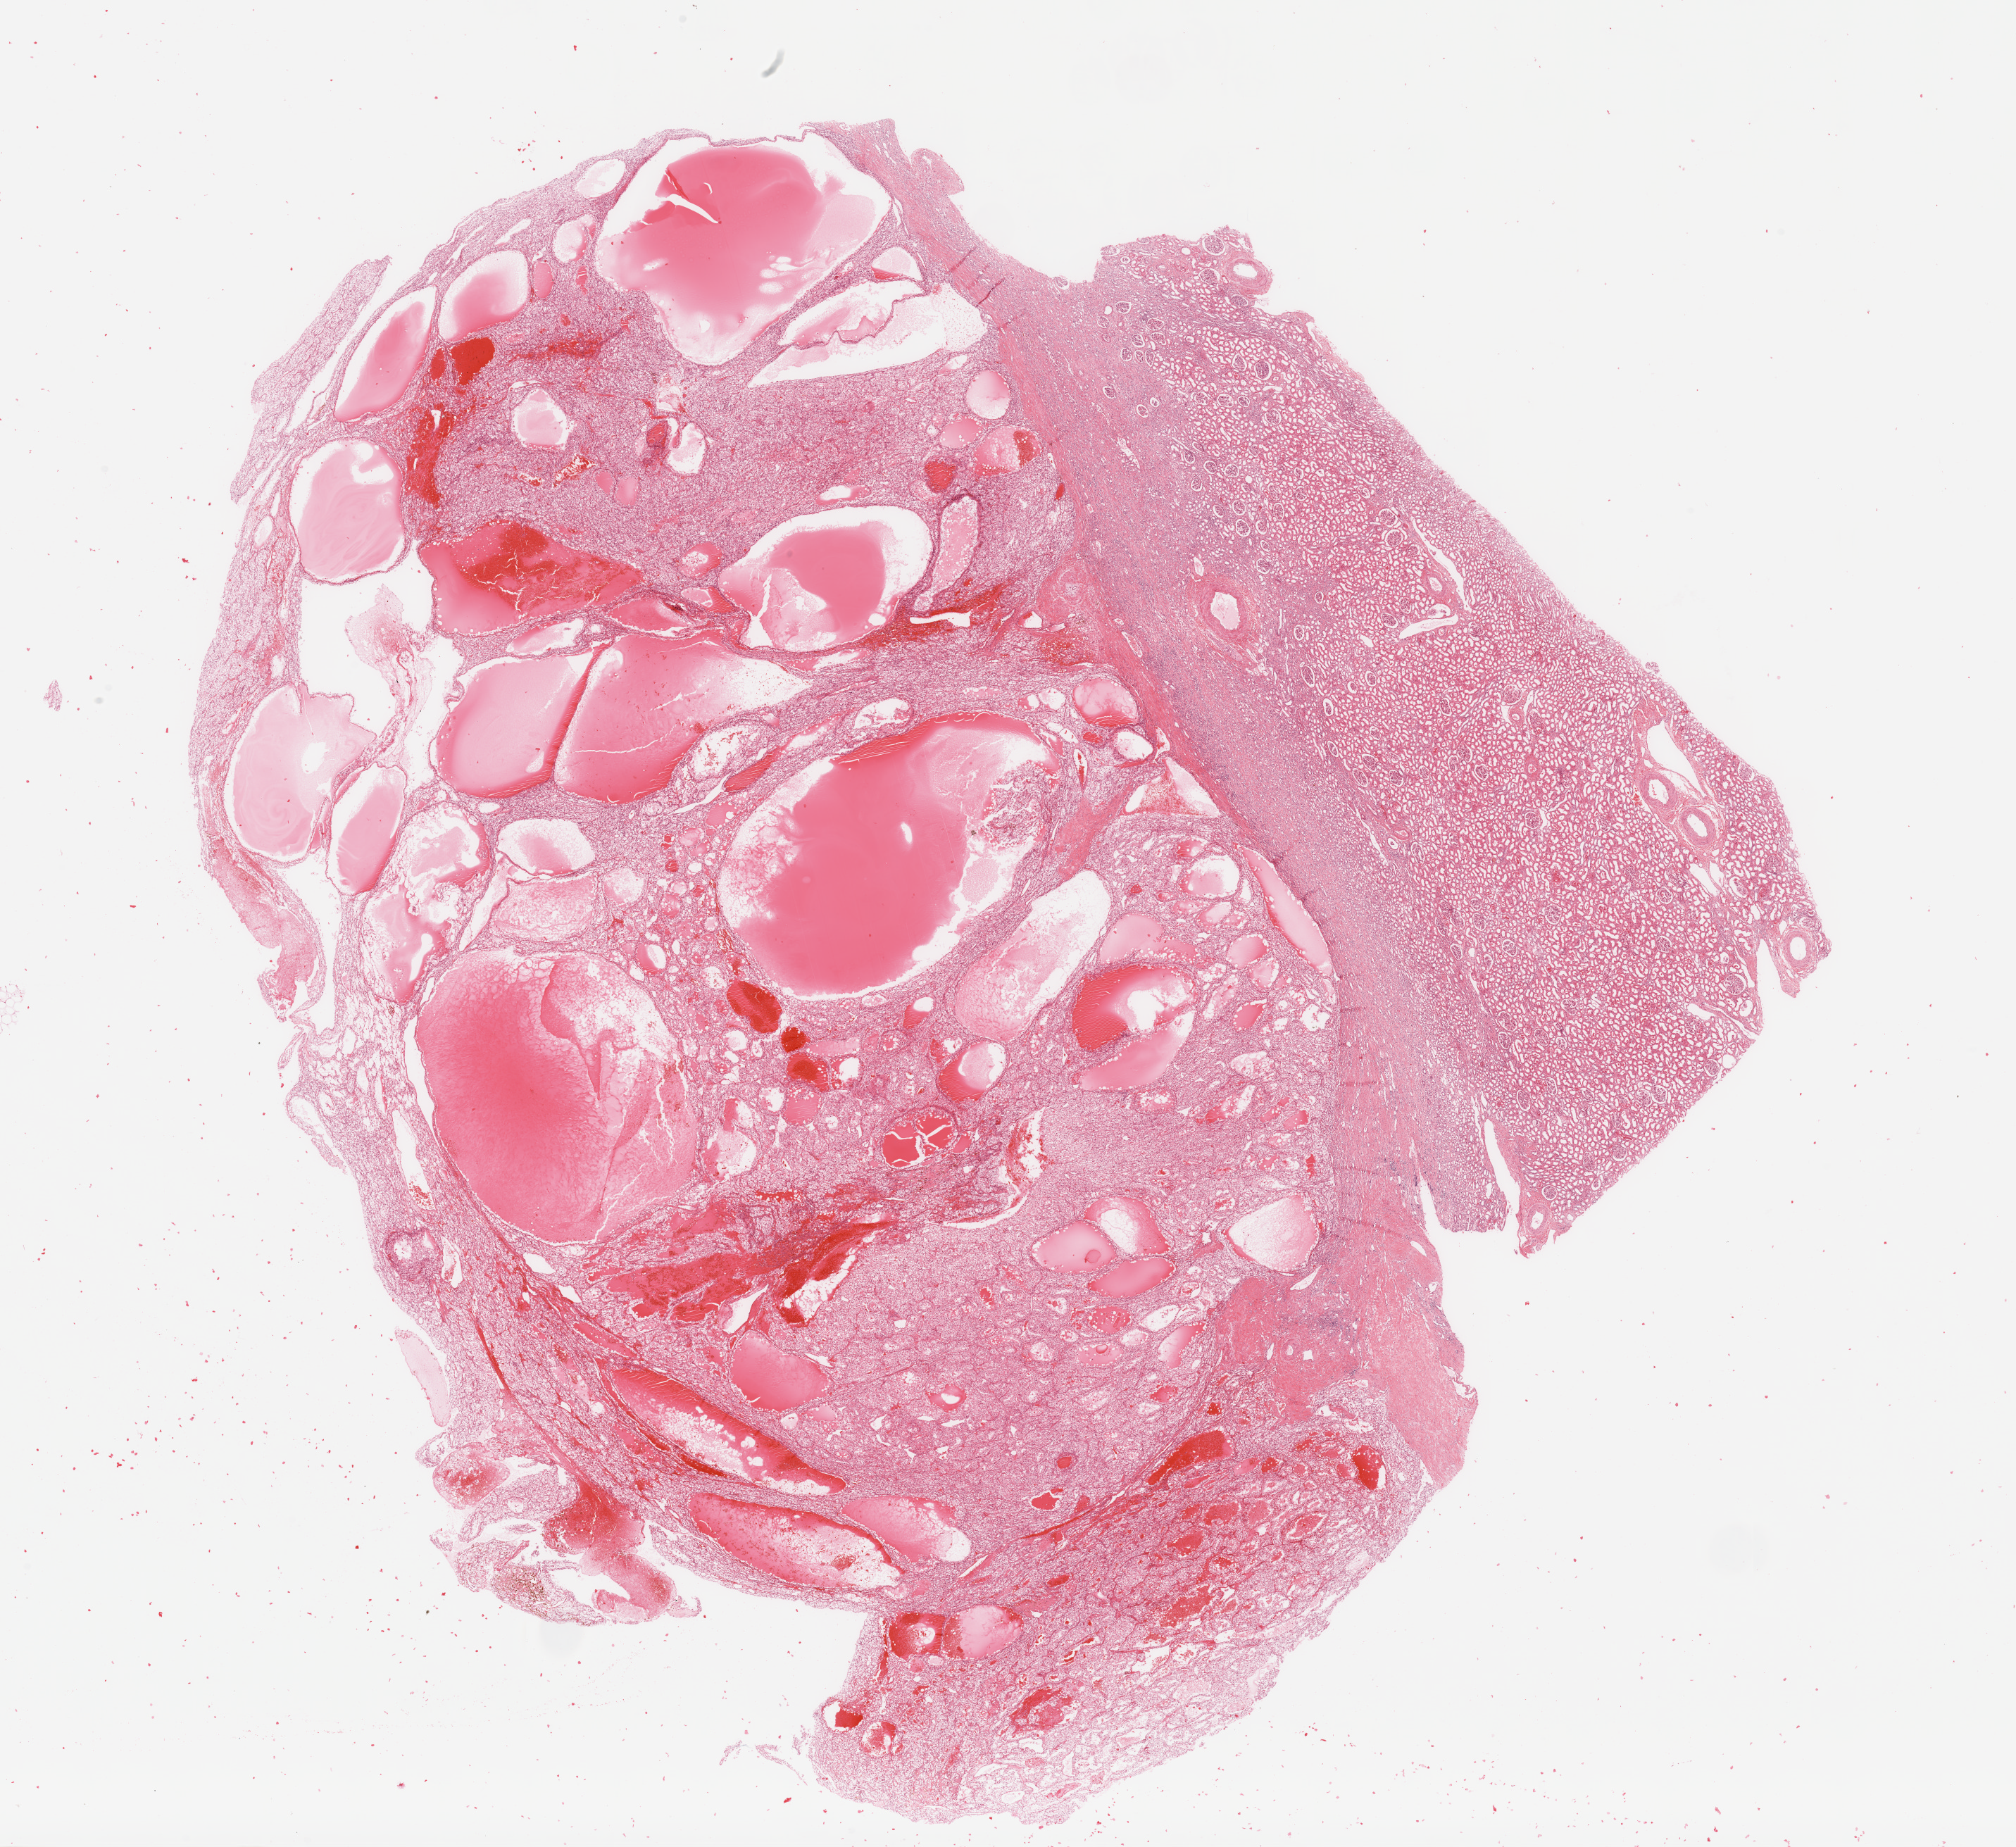
Digitized H&E tissue section (whole slide) — whole scanned area (about 22.6 x 20.7 mm, acquisition: 20x scan) shown as a low-resolution overview, tumour tissue sample, sampled site: kidney. Male, 47 y/o. Histologic grade: G3 (poorly differentiated). Slide review estimates, as recorded: tumour nuclei 65%, necrosis 5%.
AJCC pathologic stage: I. Histologic diagnosis: Renal cell carcinoma, NOS.